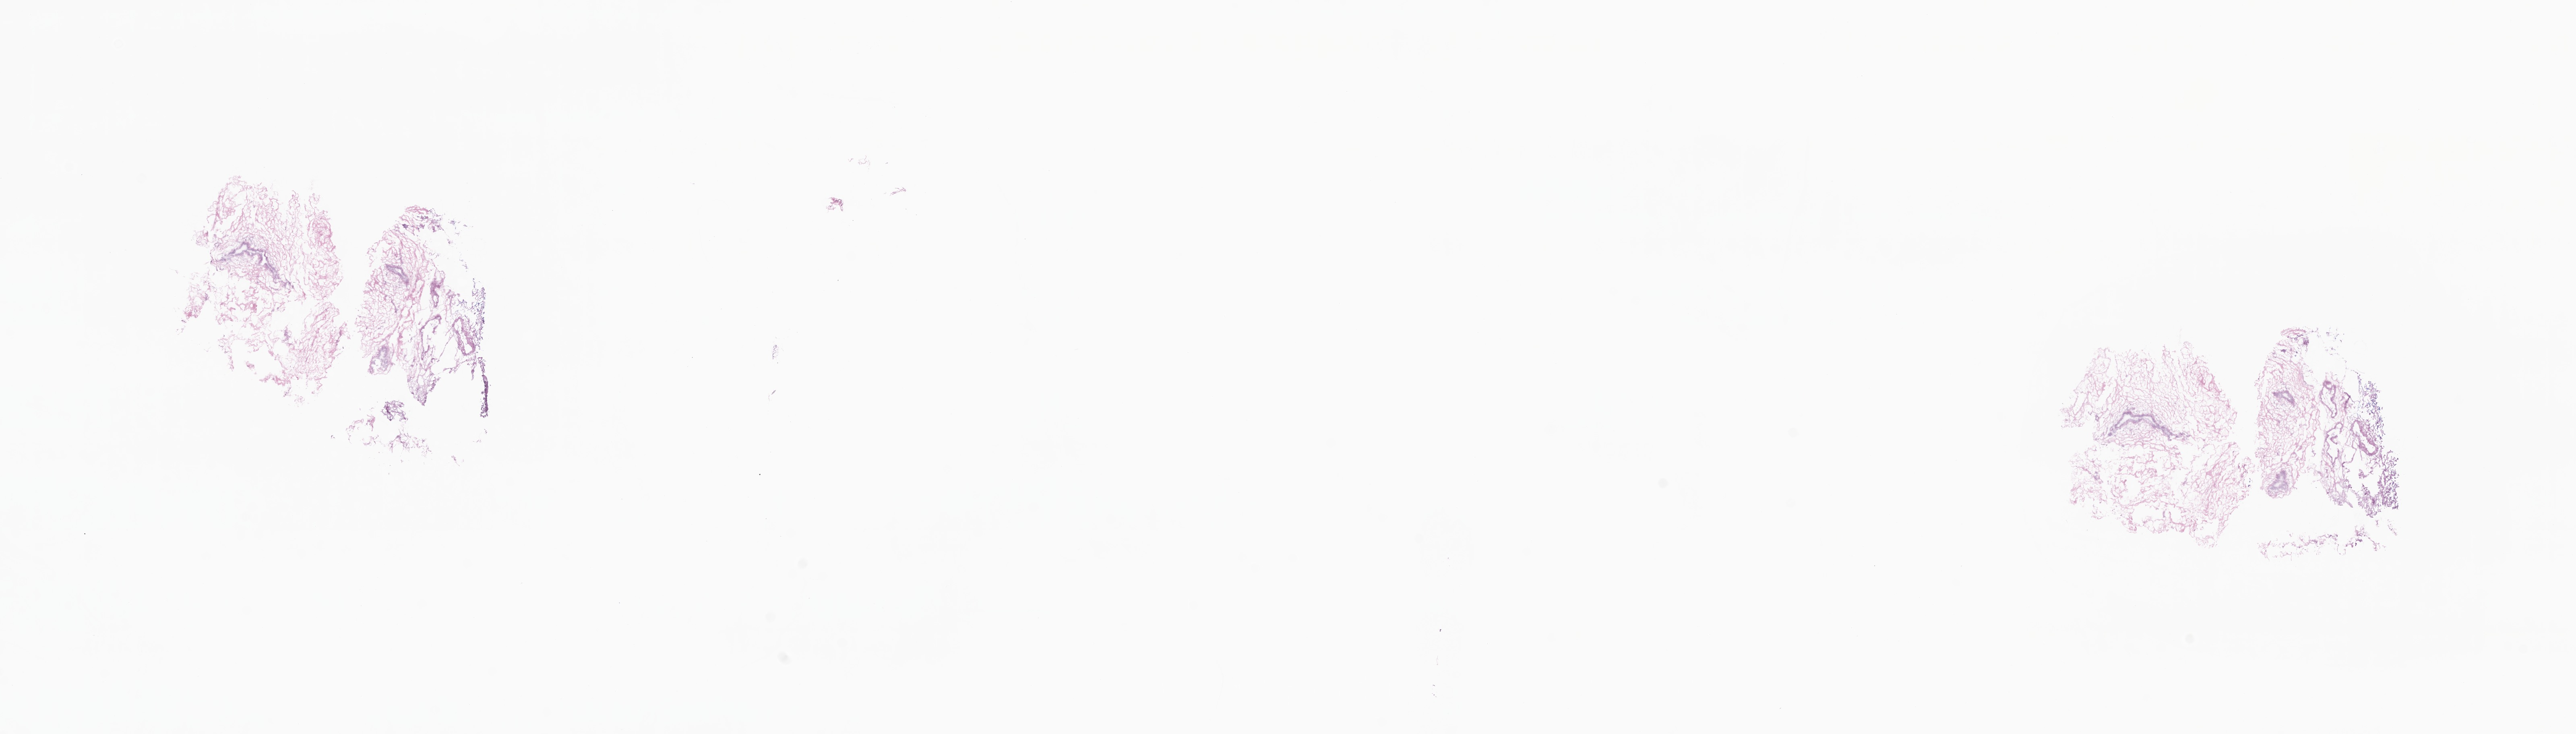
Digitized hematoxylin and eosin (H&E)-stained section, shown as a low-resolution overview of the whole scanned area (about 27.0 x 7.7 mm). Frozen section. Primary tumor. Anatomic site: breast. Female, age 76 years at initial diagnosis. Slide review estimates, as recorded: tumor cells 0%, tumor nuclei 0%, stromal cells 50%, necrosis 0%, normal cells 50%. Infiltration values recorded for this section: lymphocyte infiltration 3%, monocyte infiltration 2%, neutrophil infiltration 4%.
Section: top of the tissue portion. Histologic diagnosis: Infiltrating duct carcinoma, NOS.